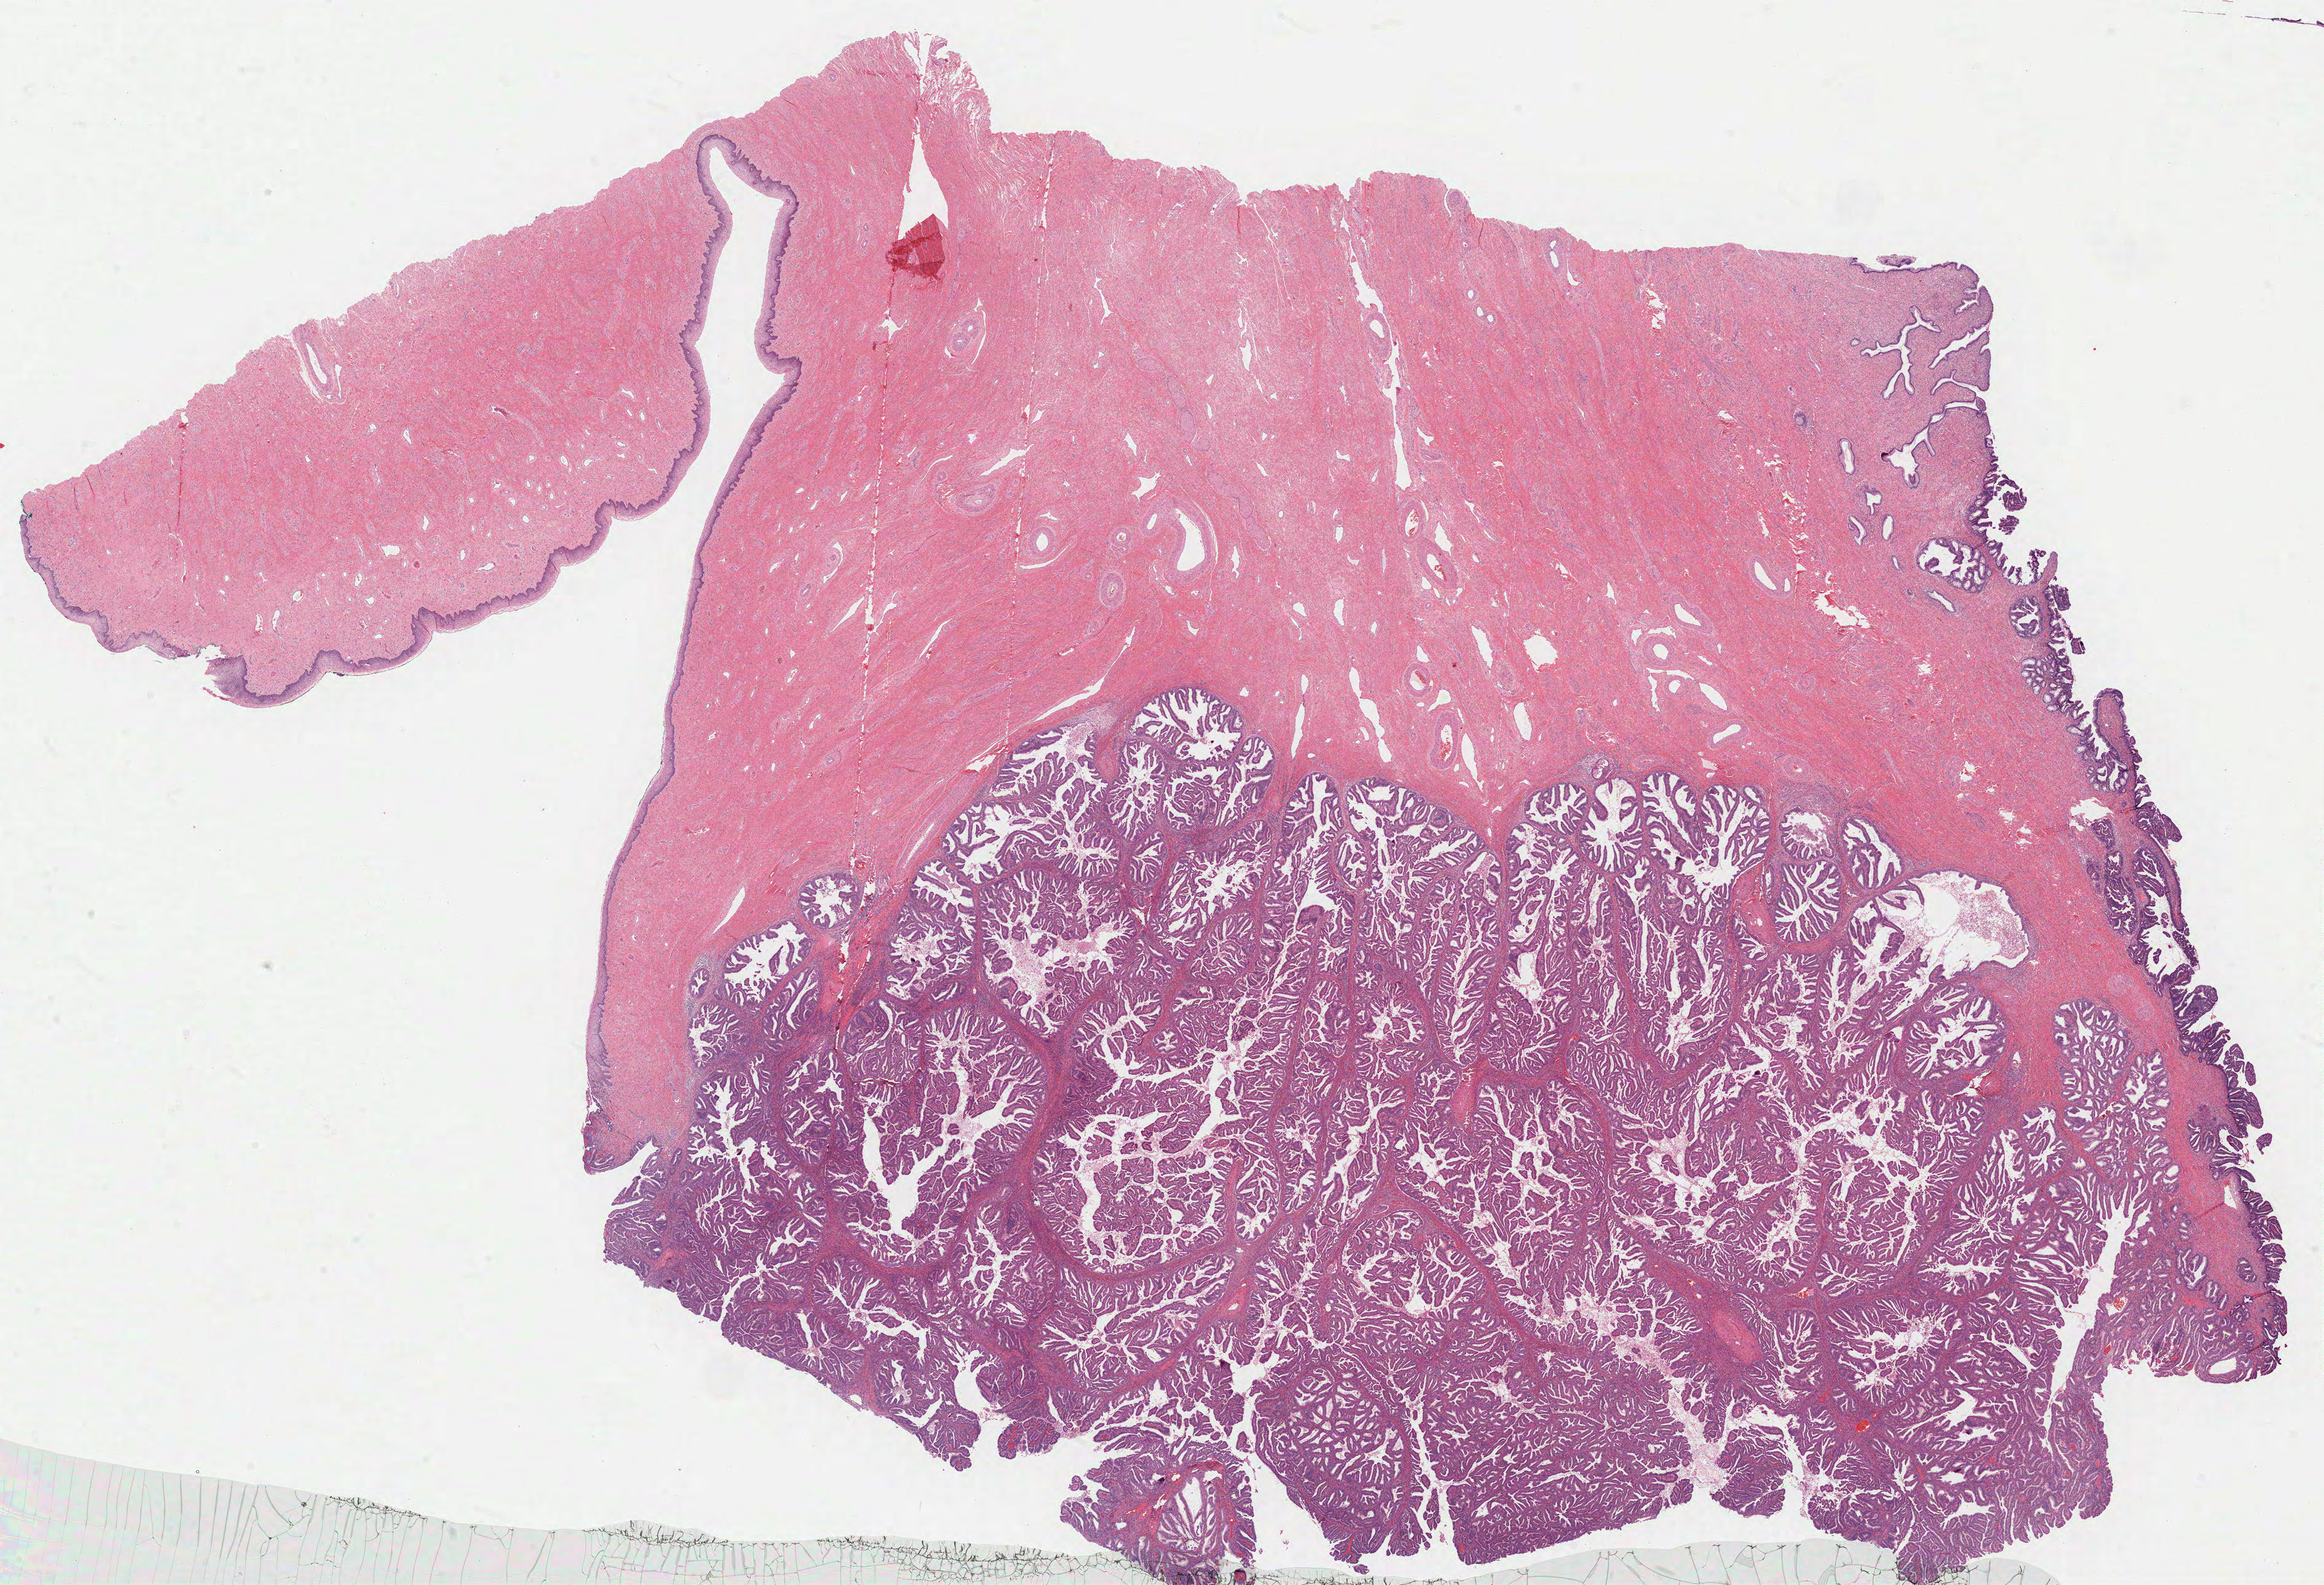
H&E-stained whole-slide image, whole scanned area (about 29.7 x 20.3 mm, from a 40x scan) shown as a low-resolution overview, FFPE section, primary tumour sample from the cervix. Female patient; age at initial diagnosis 44 years.
Histologic diagnosis: Endometrioid adenocarcinoma, NOS (endocervix).